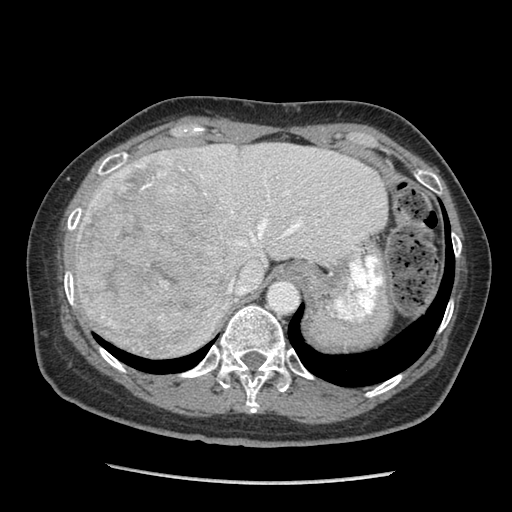
Contrast-enhanced abdominal CT (liver protocol), one axial slice. Position 68 of 105 along the scan axis. 140 kVp. Soft-tissue window (W 400 / L 40 HU). 2.5 mm slice thickness. 512 × 512 image matrix, field of view 340 × 340 mm. From the clinical record (not read from this slice): diagnosis: hepatocellular carcinoma (patient treated with transarterial chemoembolisation; whether this scan precedes or follows treatment is not stated here); TNM stage (as recorded): Stage-I; Child-Pugh class: A; tumour differentiation: moderately differentiated; tumour nodularity: uninodular.
Structures marked on this image (semi-automatic segmentation, software-assisted and operator-edited):
- abdominal aorta: bounding box [x1, y1, x2, y2] px = [269, 280, 298, 313]
- liver parenchyma outside the tumour (the mass and vessels are separate outlines, so this box may not span the whole liver): [74, 142, 388, 352]
- mass: [73, 154, 229, 357]
- liver vessels: [137, 165, 302, 292]